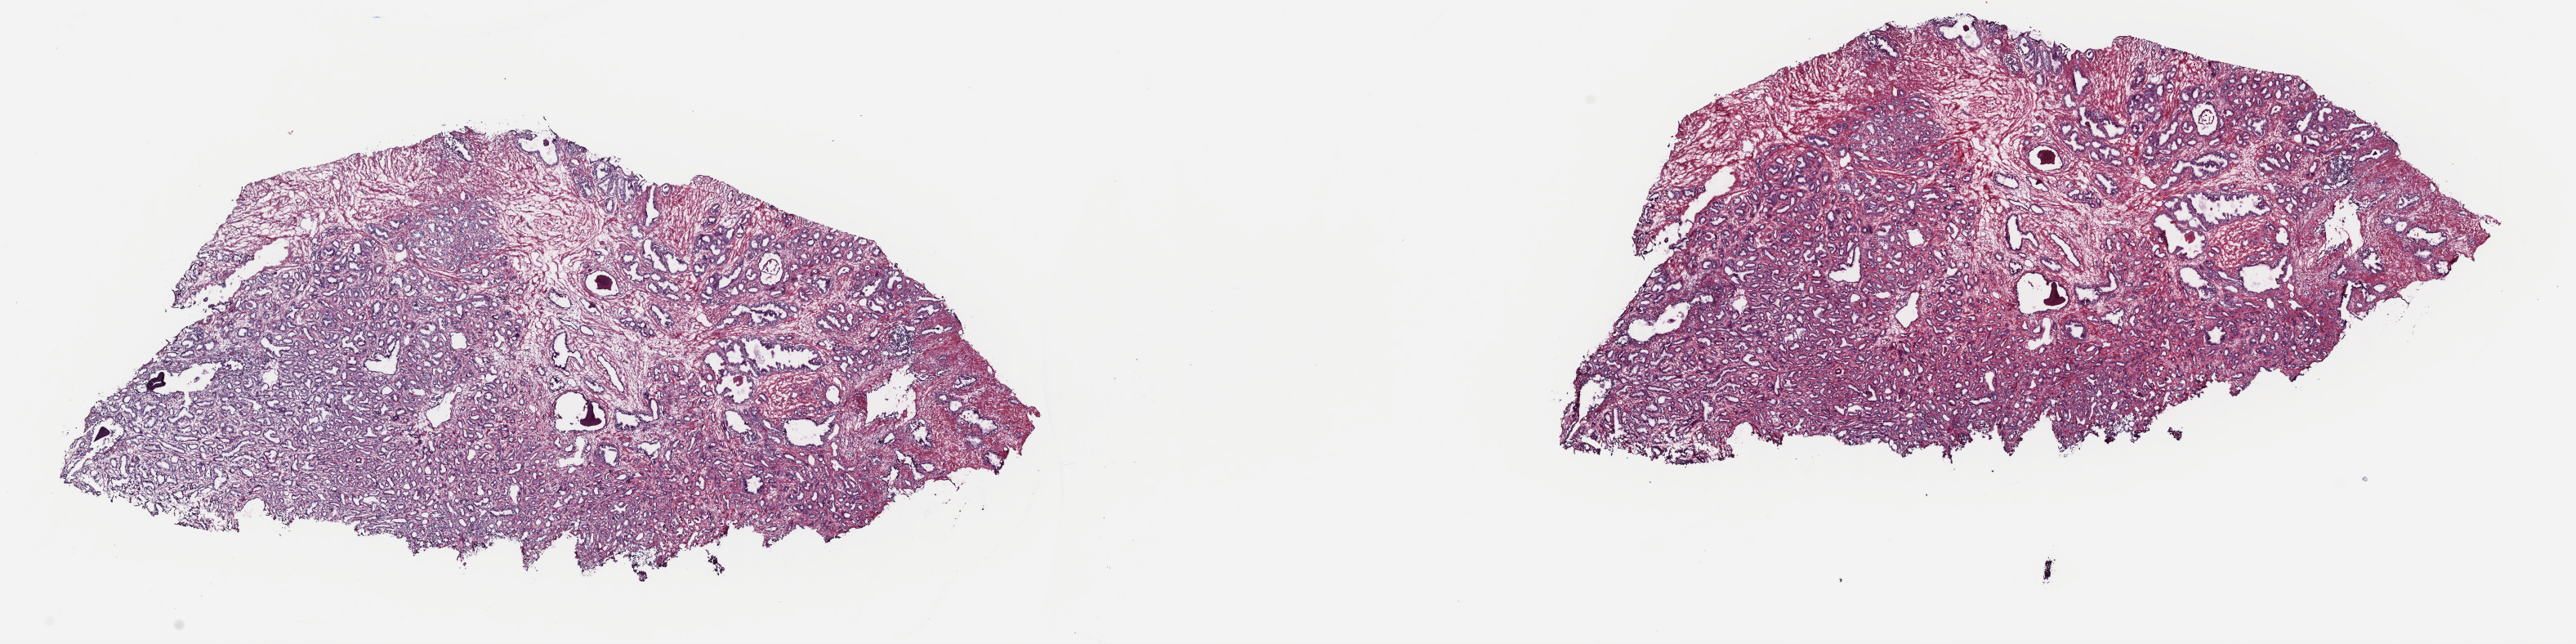
Whole-slide histology image, H&E-stained — low-resolution overview of the scanned area, about 24.9 x 6.2 mm; frozen section; primary tumour sample from the prostate. Male patient; age at initial diagnosis 66 years. Gleason score: 6 (3+3). Pathologist review of this section (percent, as recorded): tumour cells 45%, tumour nuclei 80%, normal cells 5%, stromal cells 47%, necrosis 3%. Inflammatory infiltration, as recorded: lymphocyte infiltration 3%, monocyte infiltration 0%, neutrophil infiltration 0%.
Pathologic diagnosis: Adenocarcinoma, NOS (prostate gland). Laterality: right. Lymph nodes positive (case pathology): 0 of 2 examined.